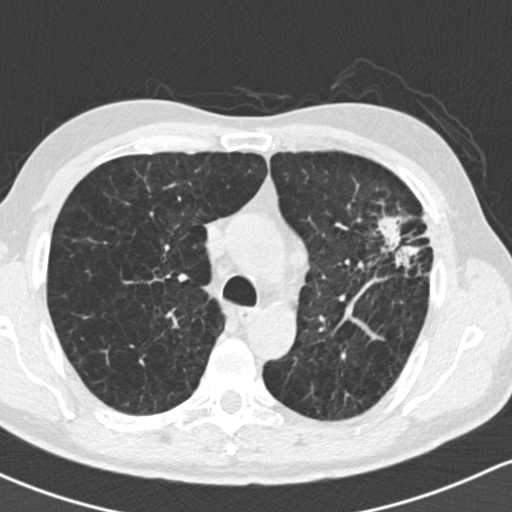
Low-dose screening chest CT, one axial slice. Slice 109 of 162 in the series (ordered by position). Reconstruction kernel B30f. 120 kVp. Lung window (W 1500 / L -600 HU). 2 mm slice thickness. 512 × 512 image matrix, field of view 318 × 318 mm.
Annotated regions visible in this slice (manually delineated by an expert):
- lesion 1 (tumor, upper lobe of left lung): bounding box (x1, y1, x2, y2) in pixels: (377, 215, 420, 269)